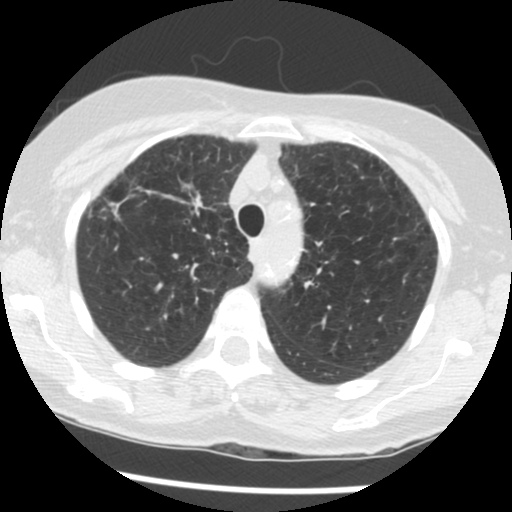
Low-dose screening chest CT, one axial slice. Slice 97 of 124 in the series (ordered by position). 120 kVp. Lung window (W 1500 / L -600 HU). 2.5 mm slice thickness. 512 × 512 image matrix, field of view 290 × 290 mm.
Structures marked on this image (manually delineated by an expert):
- lesion 1 (tumor, upper lobe of right lung): bounding box [x1, y1, x2, y2] px = [192, 195, 203, 210]